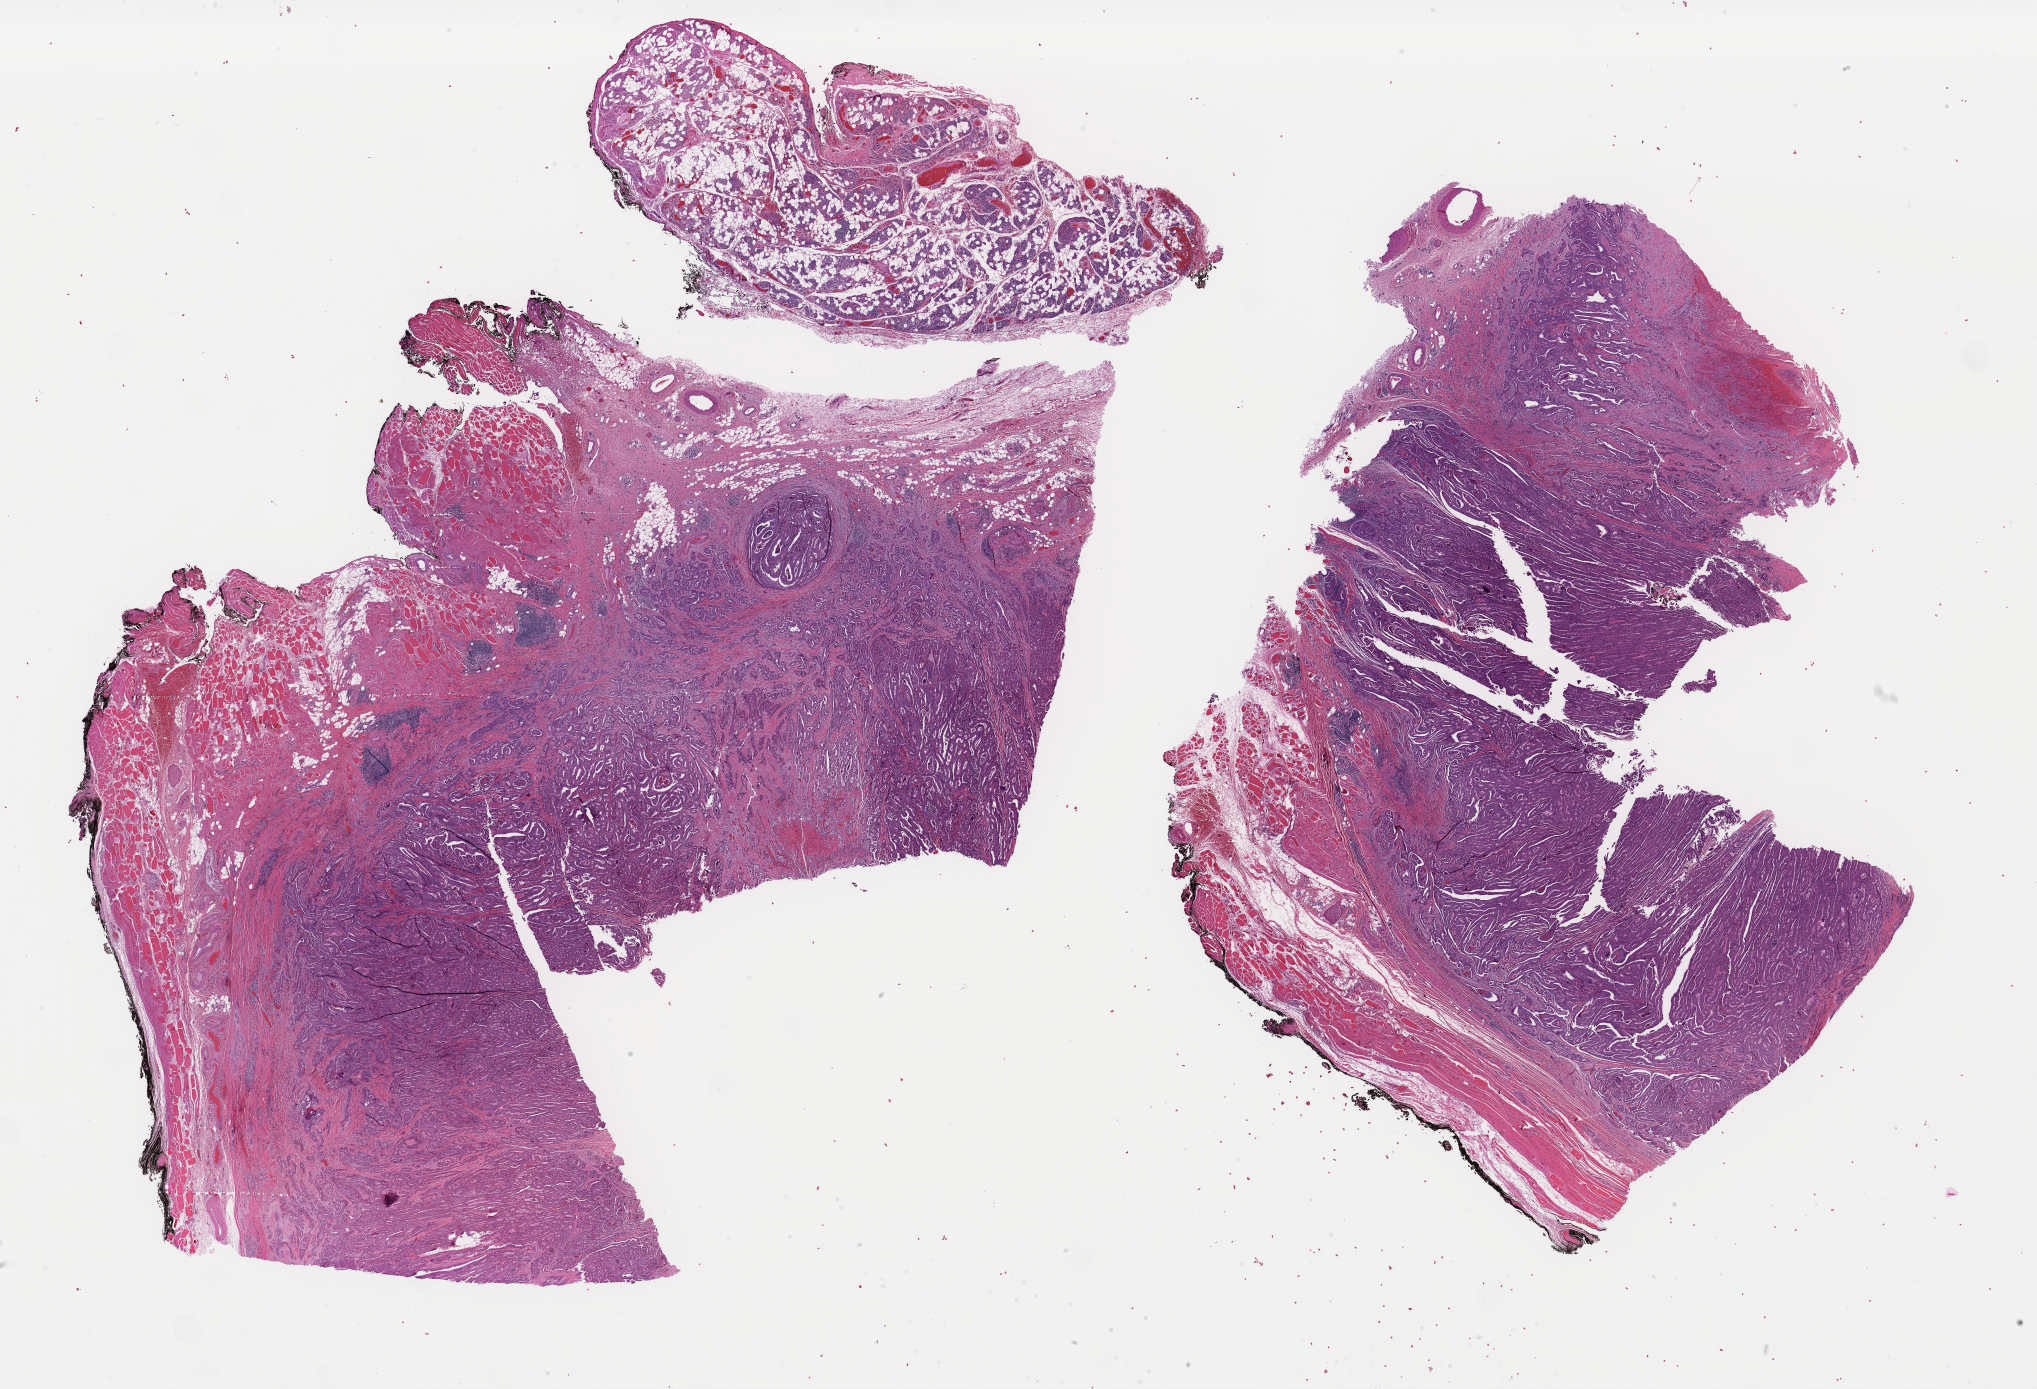
H&E whole-slide image — low-resolution overview of the scanned area, about 32.2 x 21.9 mm. FFPE section. Primary tumour sample from the thyroid. Female, age 58 years at initial diagnosis.
AJCC pathologic stage: III (7th edition). Lymph nodes positive (case pathology): 4 of 33 examined. Diagnosis: Papillary carcinoma, columnar cell. Laterality: right.